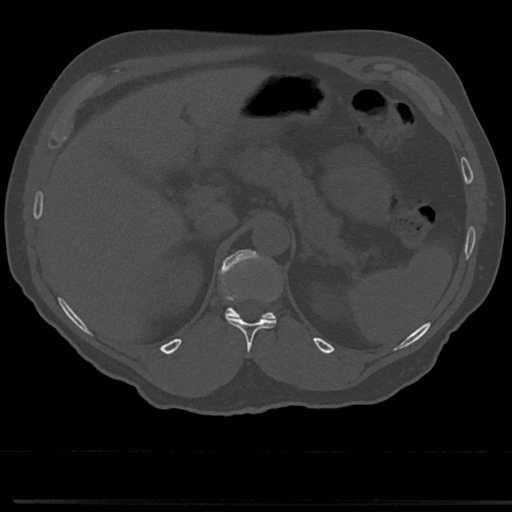
CT including the spine, one axial slice. Position 178 of 817 along the scan axis. Reconstruction kernel Br40s/3. 120 kVp. Bone window (W 1800 / L 400 HU). 0.5 mm slice thickness. 512 × 512 image matrix, field of view 355 × 355 mm. Patient: male, 61 years. From the clinical record (not read from this slice): primary cancer: prostate.
Outlined on this slice (semi-automatic segmentation, software-assisted and operator-edited):
- T11 vertebra: bounding box (x1, y1, x2, y2) in pixels: (226, 317, 276, 353)
- T12 vertebra: (219, 249, 276, 321)